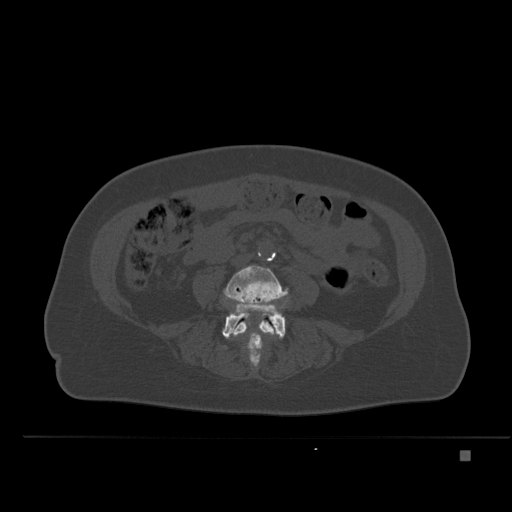
CT including the spine, one axial slice. Slice 171 of 477 in the series (ordered by position). Bone window (W 1800 / L 400 HU). 512 × 512 image matrix. Female patient, age 74 years. Case-level facts recorded for this patient, not image findings: primary cancer: colon.
Annotated regions visible in this slice (semi-automatically segmented with operator editing):
- L4 vertebra: box from (x=225, y=265) to (x=288, y=356) px
- L5 vertebra: (x=222, y=302)–(x=286, y=365)